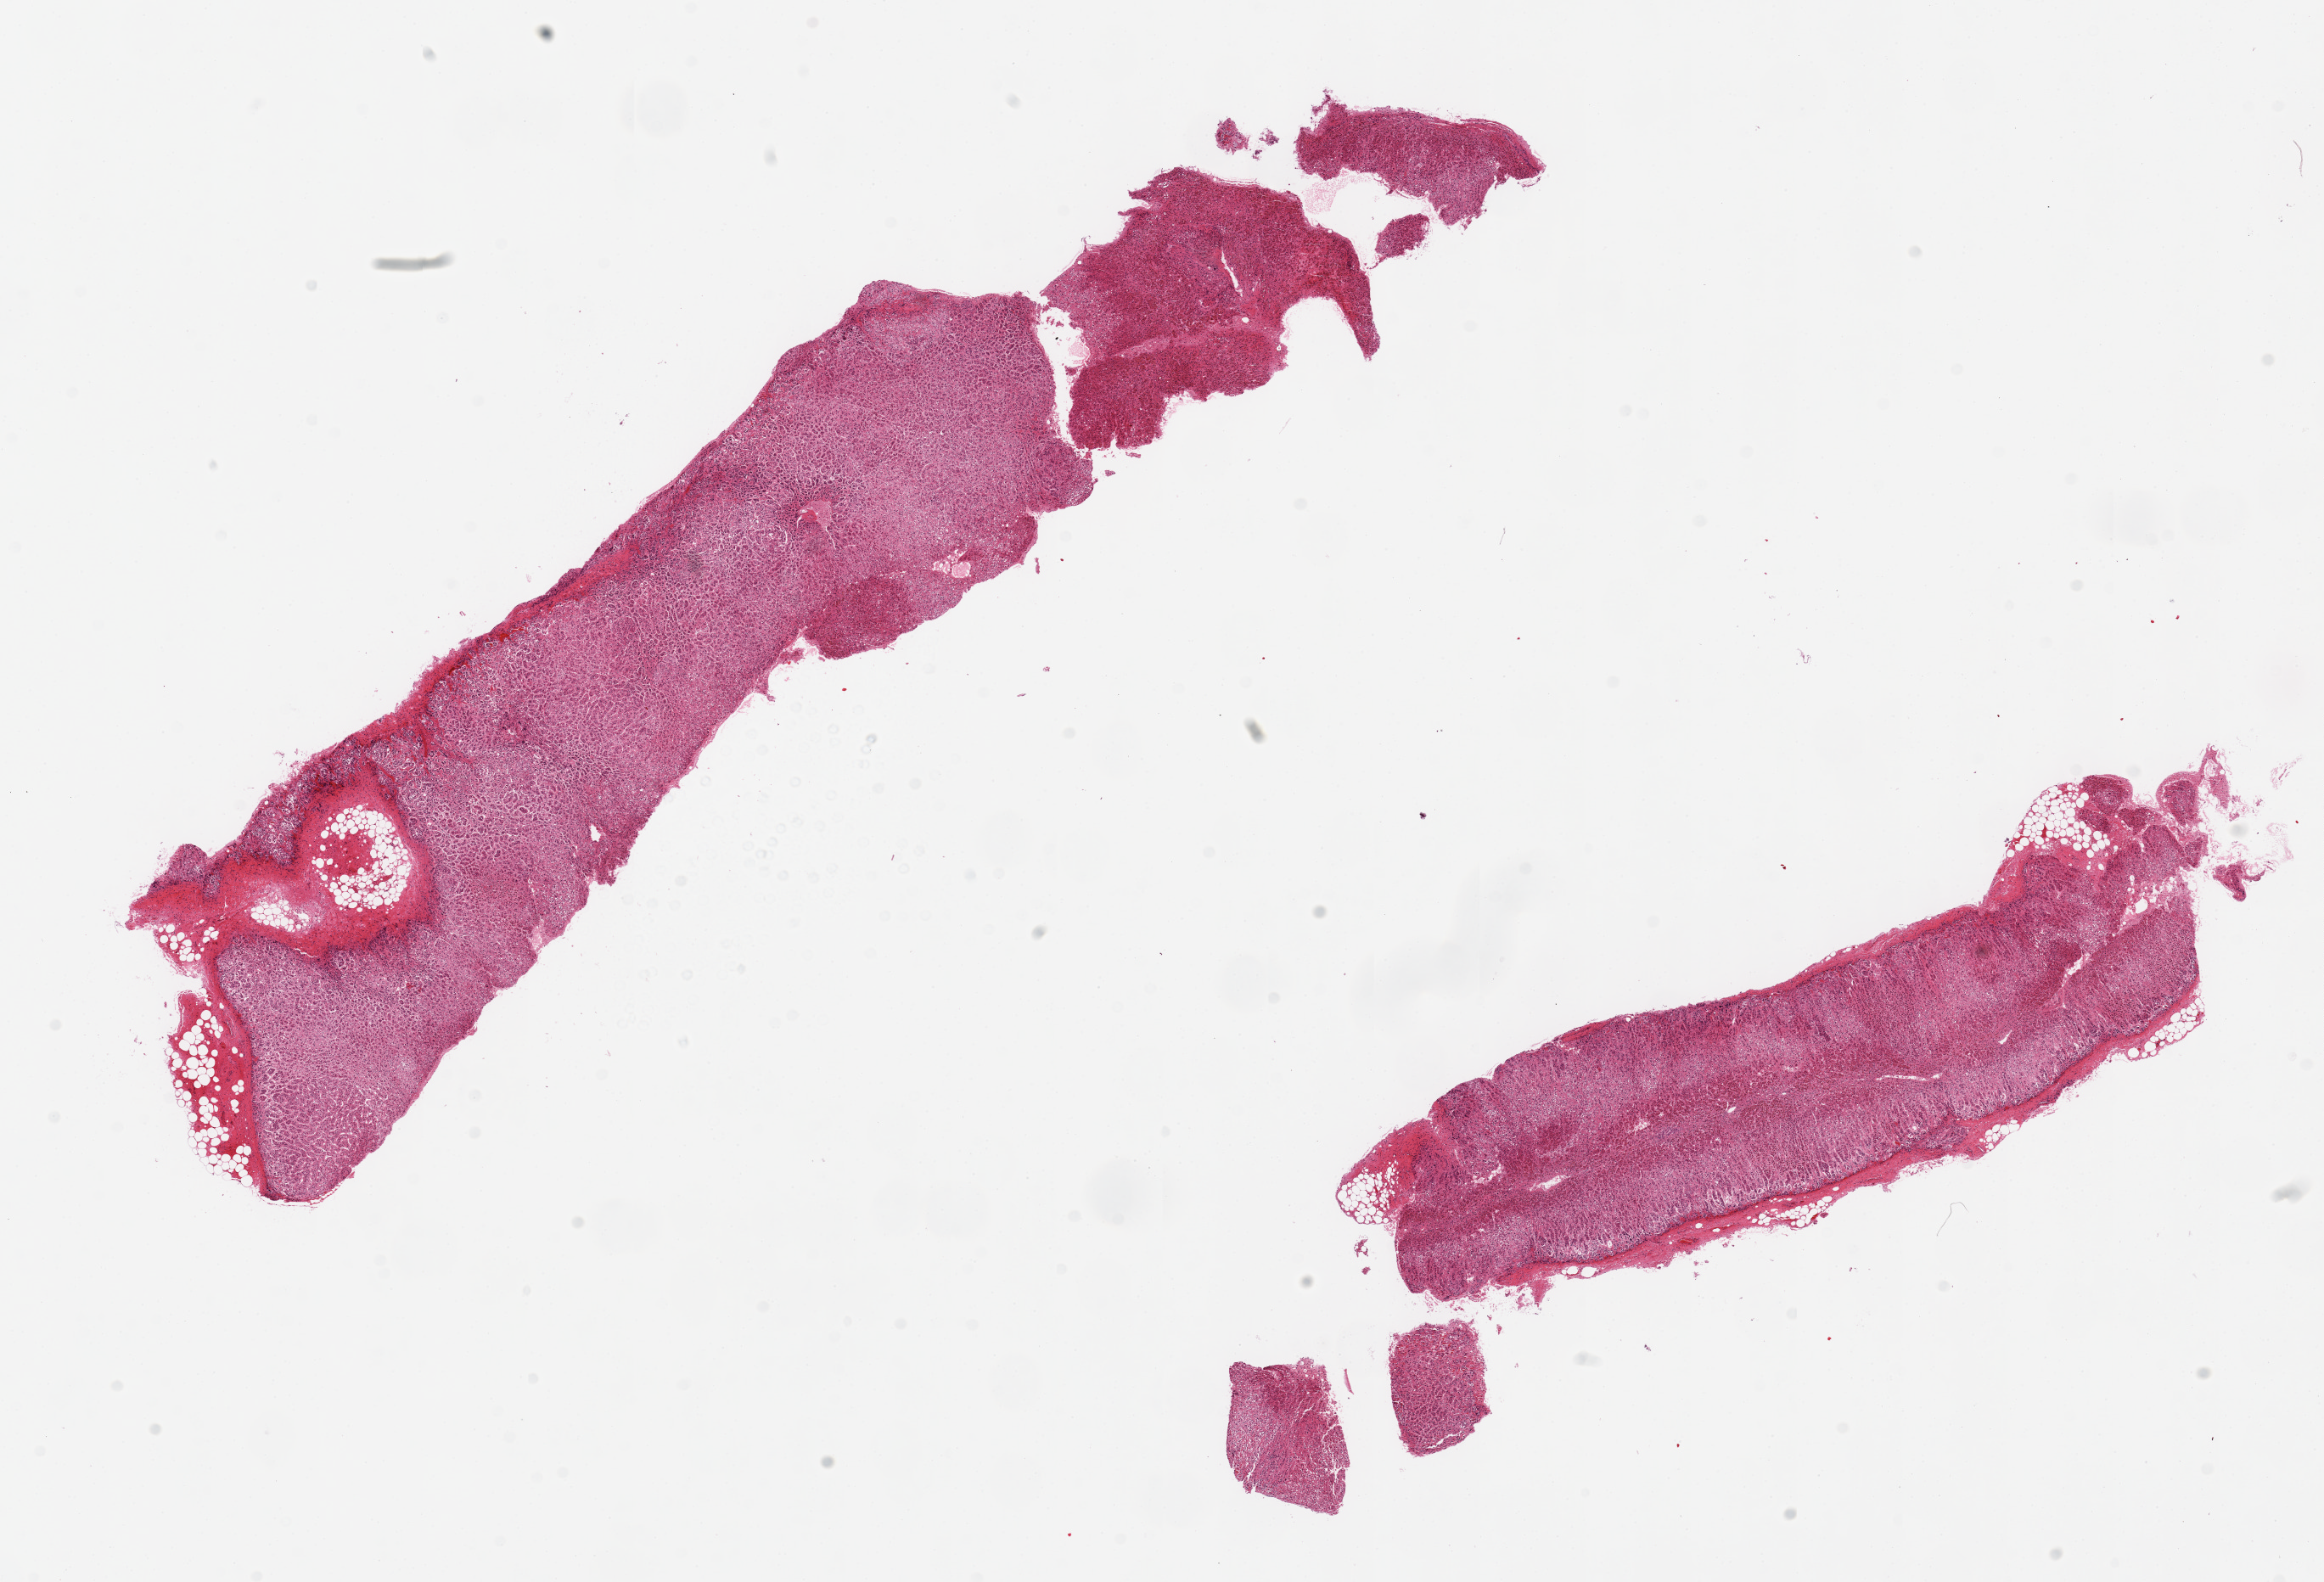
Haematoxylin and eosin whole-slide image, whole scanned area (about 21.7 x 14.7 mm, from a 20x scan) shown as a low-resolution overview; PAXgene-fixed, paraffin-embedded tissue; target tissue: adrenal gland; donor tissue sample. Male donor.
• pathologist's review note for this sample: 2 pieces